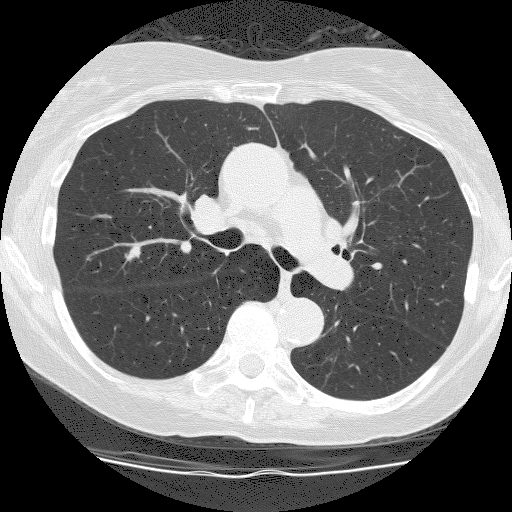
Axial slice from a low-dose chest CT screening exam, second annual screen, lung window (W 1500 / L -600 HU), 2.5 mm slice thickness, slice 70 of 186 in the series, 512 × 512 image matrix. Female participant, aged 66 years at enrolment.
Expert reader's lesion annotation, bounding box [x1, y1, x2, y2] px = [108, 231, 159, 277]. The screening reader recorded 2 non-calcified nodules or masses ≥4 mm on this exam (right upper lobe, right lower lobe); which of them this box marks is not recorded. Official screen result: positive, other. Later outcome: lung cancer diagnosed 209 days after this screen — squamous cell carcinoma, NOS, right upper lobe, stage IIIA (AJCC 6th edition), 10 mm at pathology.